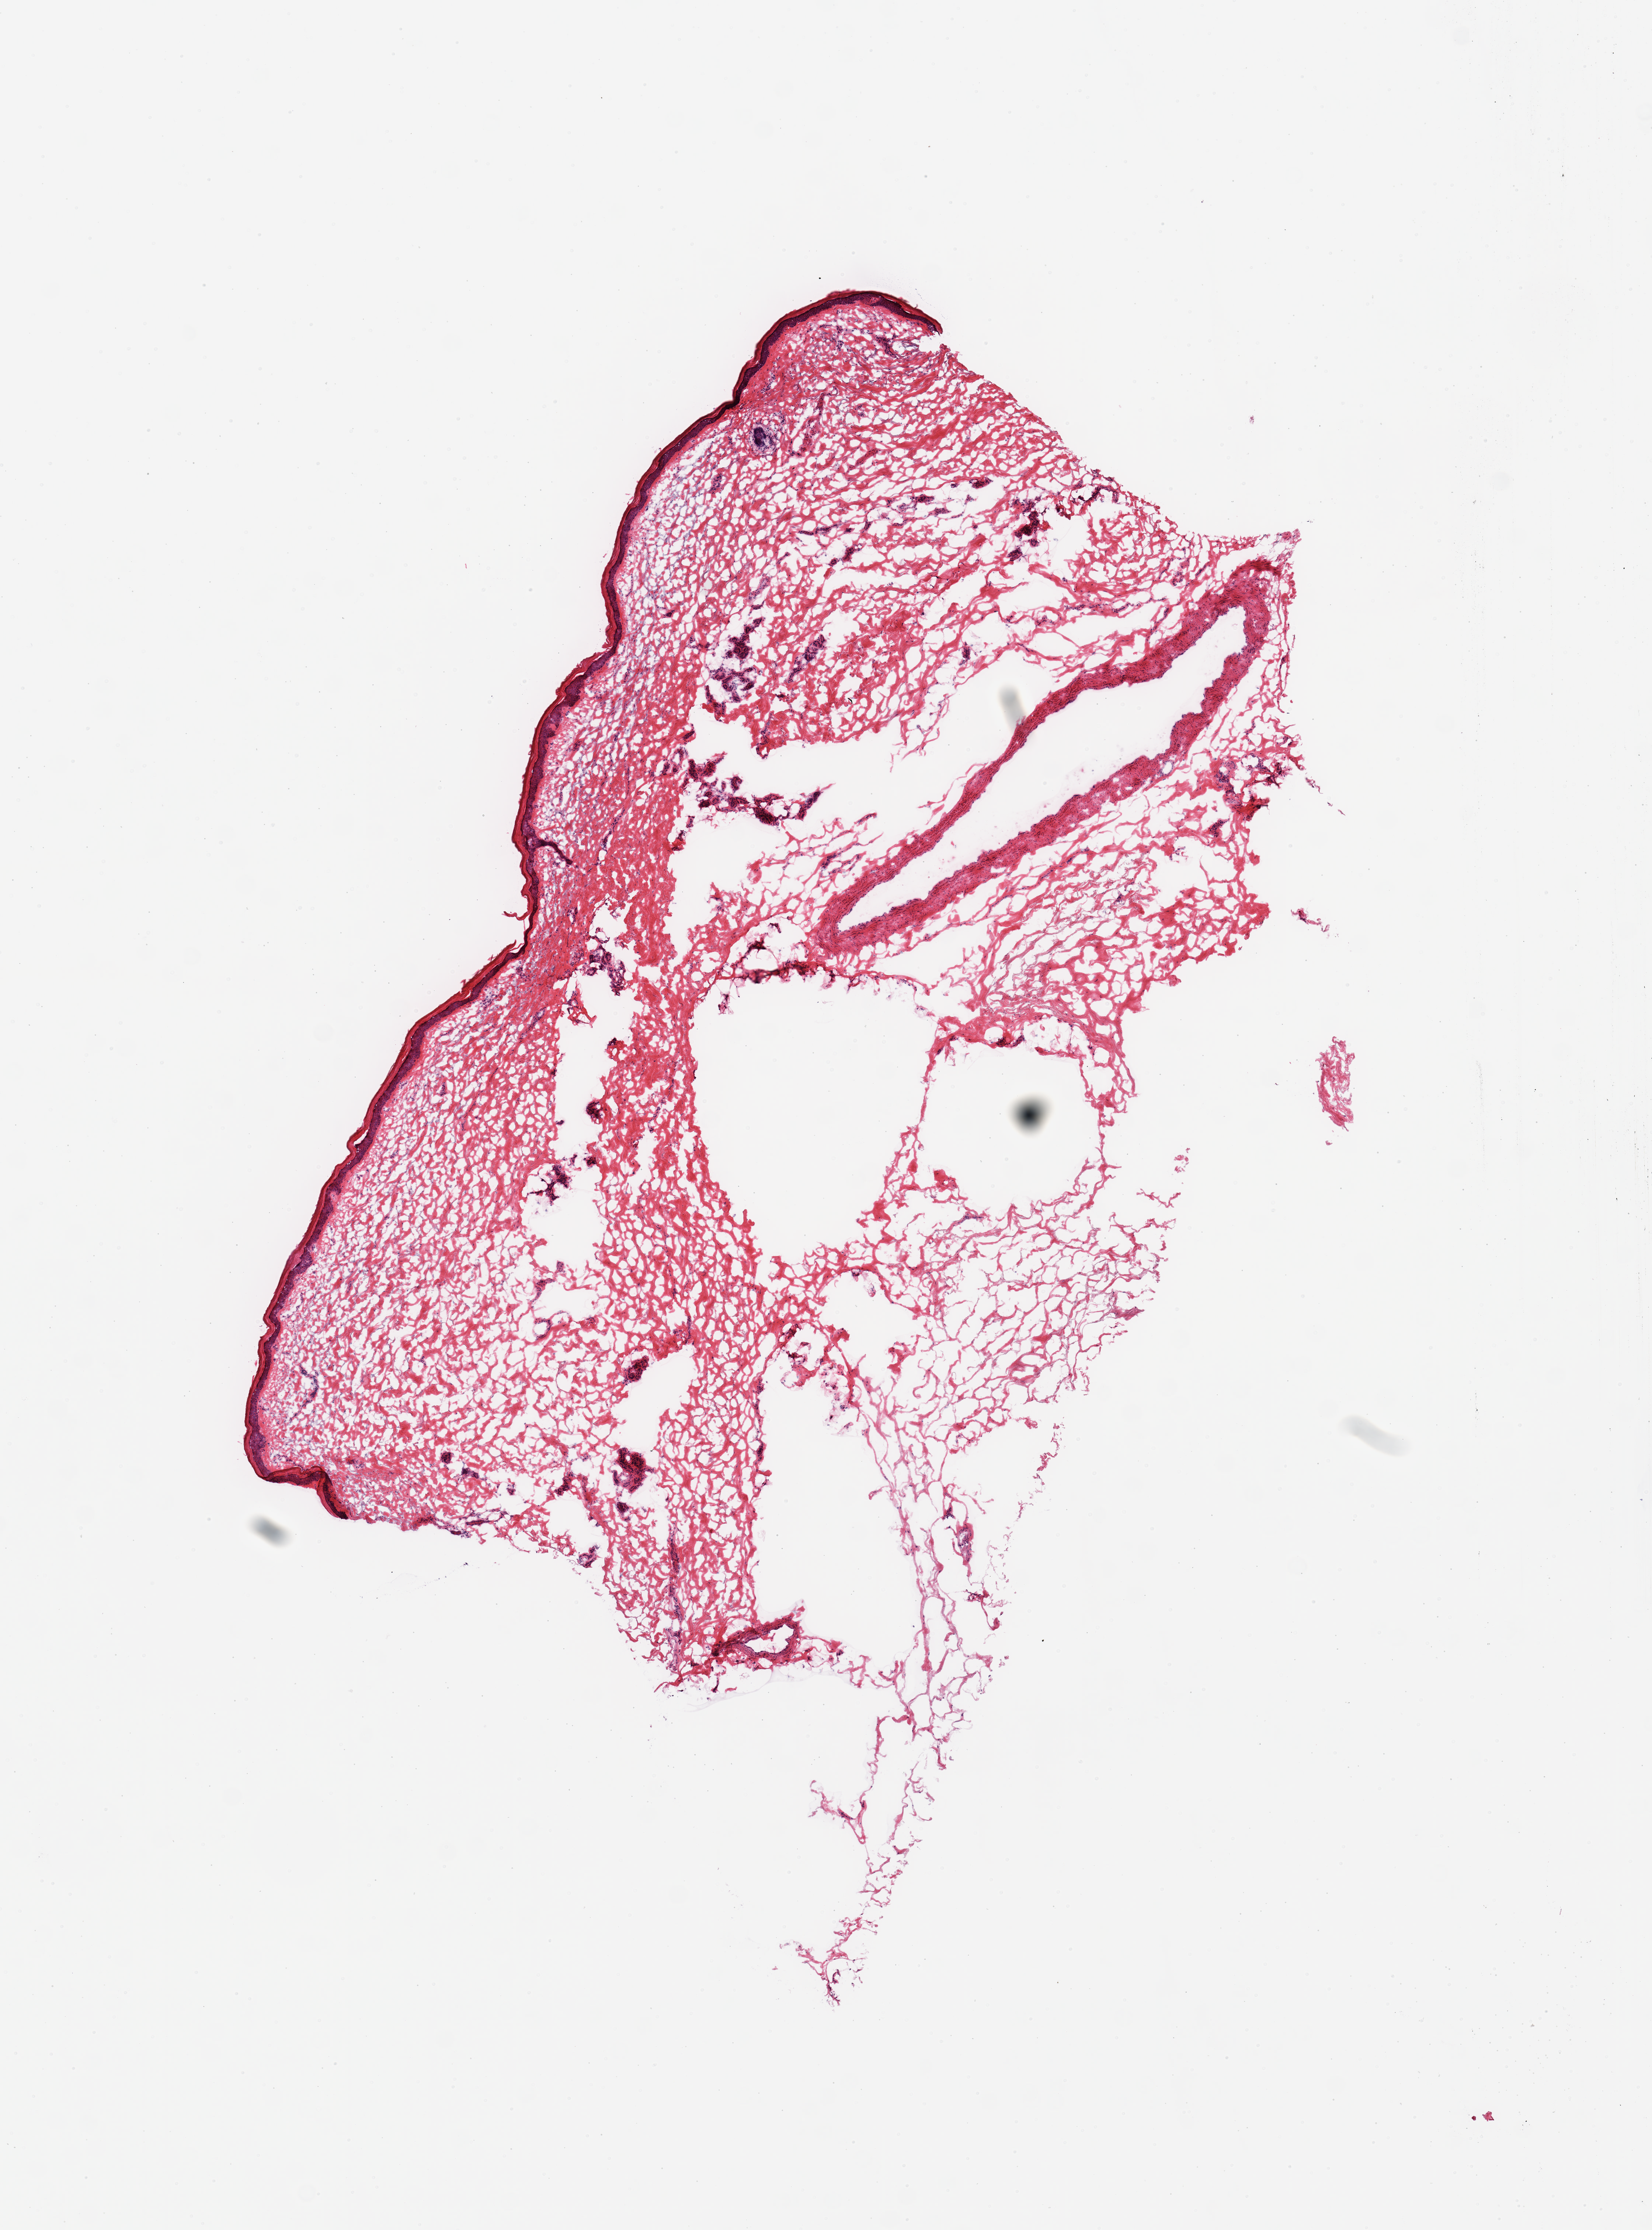
H&E whole-slide image — shown as a low-resolution overview of the whole scanned area (about 8.9 x 12.0 mm, acquisition: 20x scan); frozen section; target tissue: skin of lower leg; tissue donor sample. Donor sex: female.
Reviewer comment on this tissue sample: 1 piece; fat and artery in deep dermis.